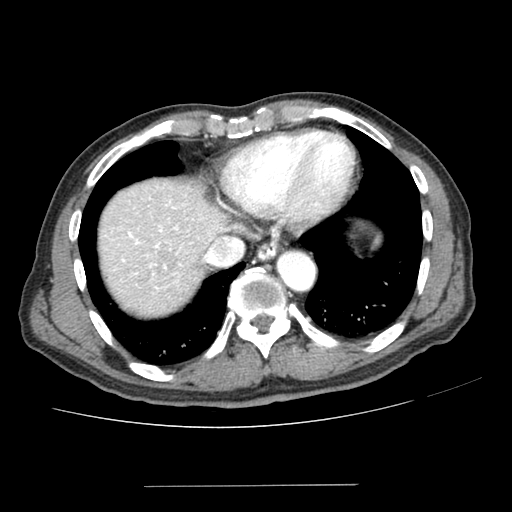
Contrast-enhanced abdominal CT (liver protocol), one axial slice; reconstruction kernel SOFT; 100 kVp; one of 2 acquisitions stored at this slice position; soft-tissue window (W 400 / L 40 HU); 2.5 mm slice thickness; 512 × 512 image matrix, field of view 360 × 360 mm. From the clinical record (not read from this slice): diagnosis: hepatocellular carcinoma (patient treated with transarterial chemoembolisation; whether this scan precedes or follows treatment is not stated here); TNM stage (as recorded): Stage-I; Child-Pugh class: A; tumour differentiation: poorly differentiated; tumour nodularity: uninodular.
Outlined on this slice (semi-automatically segmented with operator editing):
- abdominal aorta: bounding box [x1, y1, x2, y2] px = [276, 250, 314, 290]
- liver parenchyma outside the tumour (the mass and vessels are separate outlines, so this box may not span the whole liver): [100, 180, 231, 316]
- mass: [129, 246, 181, 282]
- liver vessels: [122, 201, 192, 289]